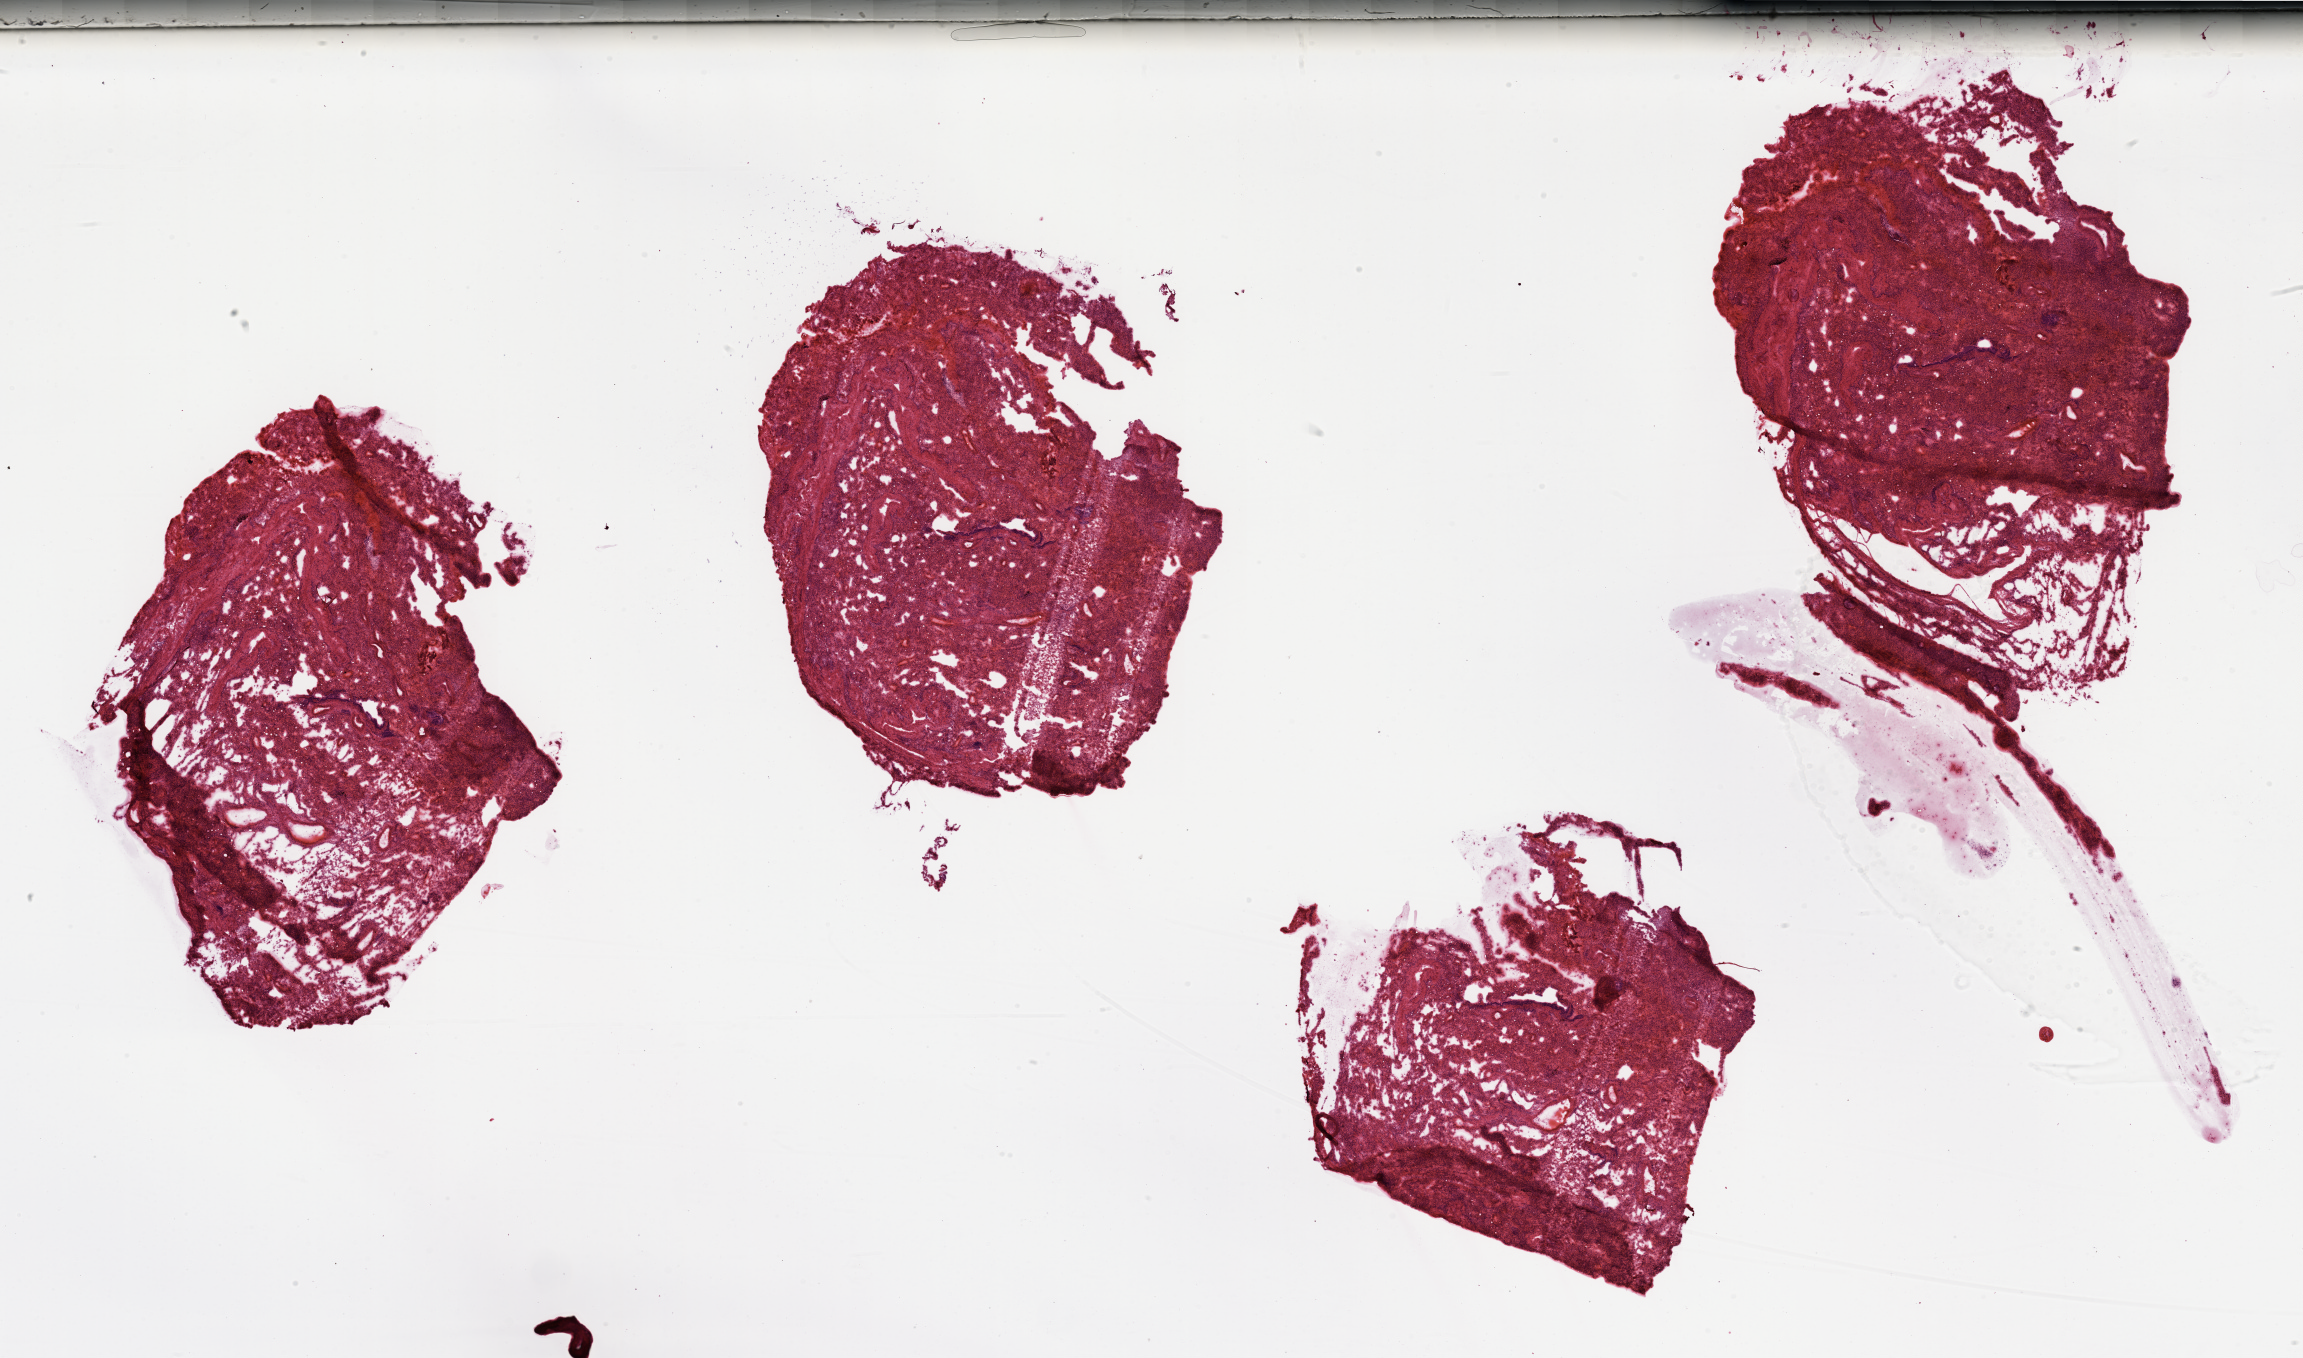
Whole-slide histology image, Hematoxylin and eosin (H&E) stained, shown as a low-resolution overview of the whole scanned area (about 36.4 x 21.5 mm, slide scanned at 20x); lung, normal (non-tumour) tissue. Male, 57 y/o.
This section: normal (non-tumour) tissue from the same patient. Patient diagnosis: Adenocarcinoma, NOS.